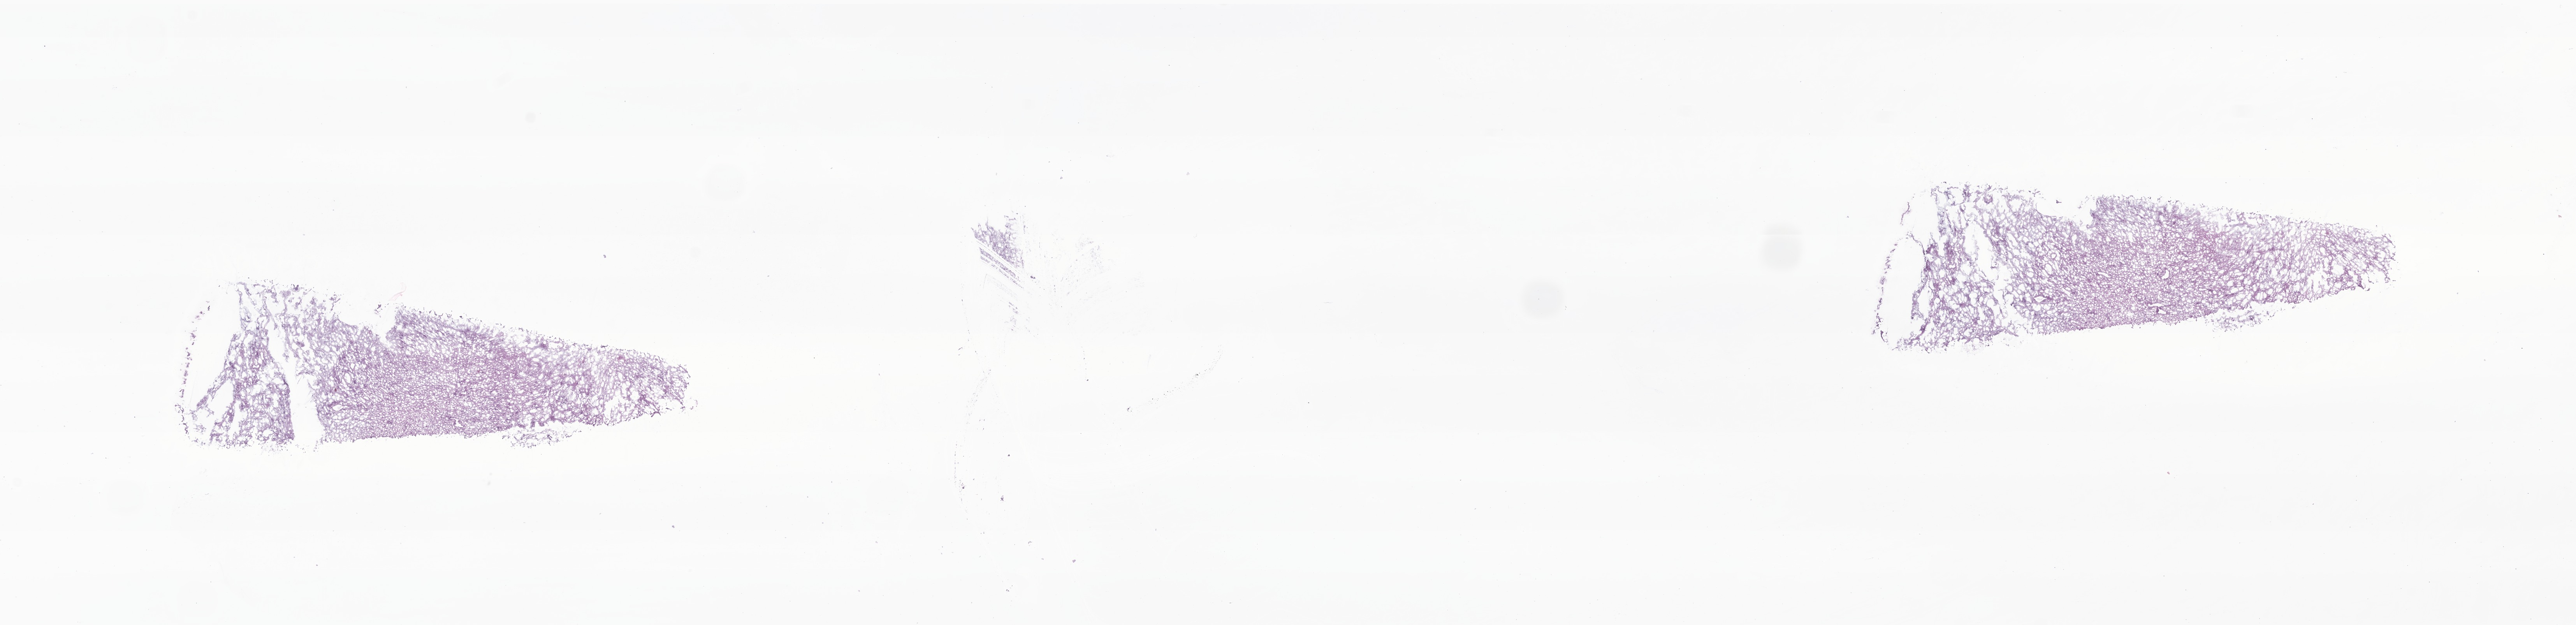
Digitized haematoxylin and eosin-stained section of tumor tissue from the brain — low-resolution overview of the scanned area, about 27.9 x 6.8 mm; frozen section. Patient: female, age 184 months.
Recorded diagnosis: Glioma, malignant.